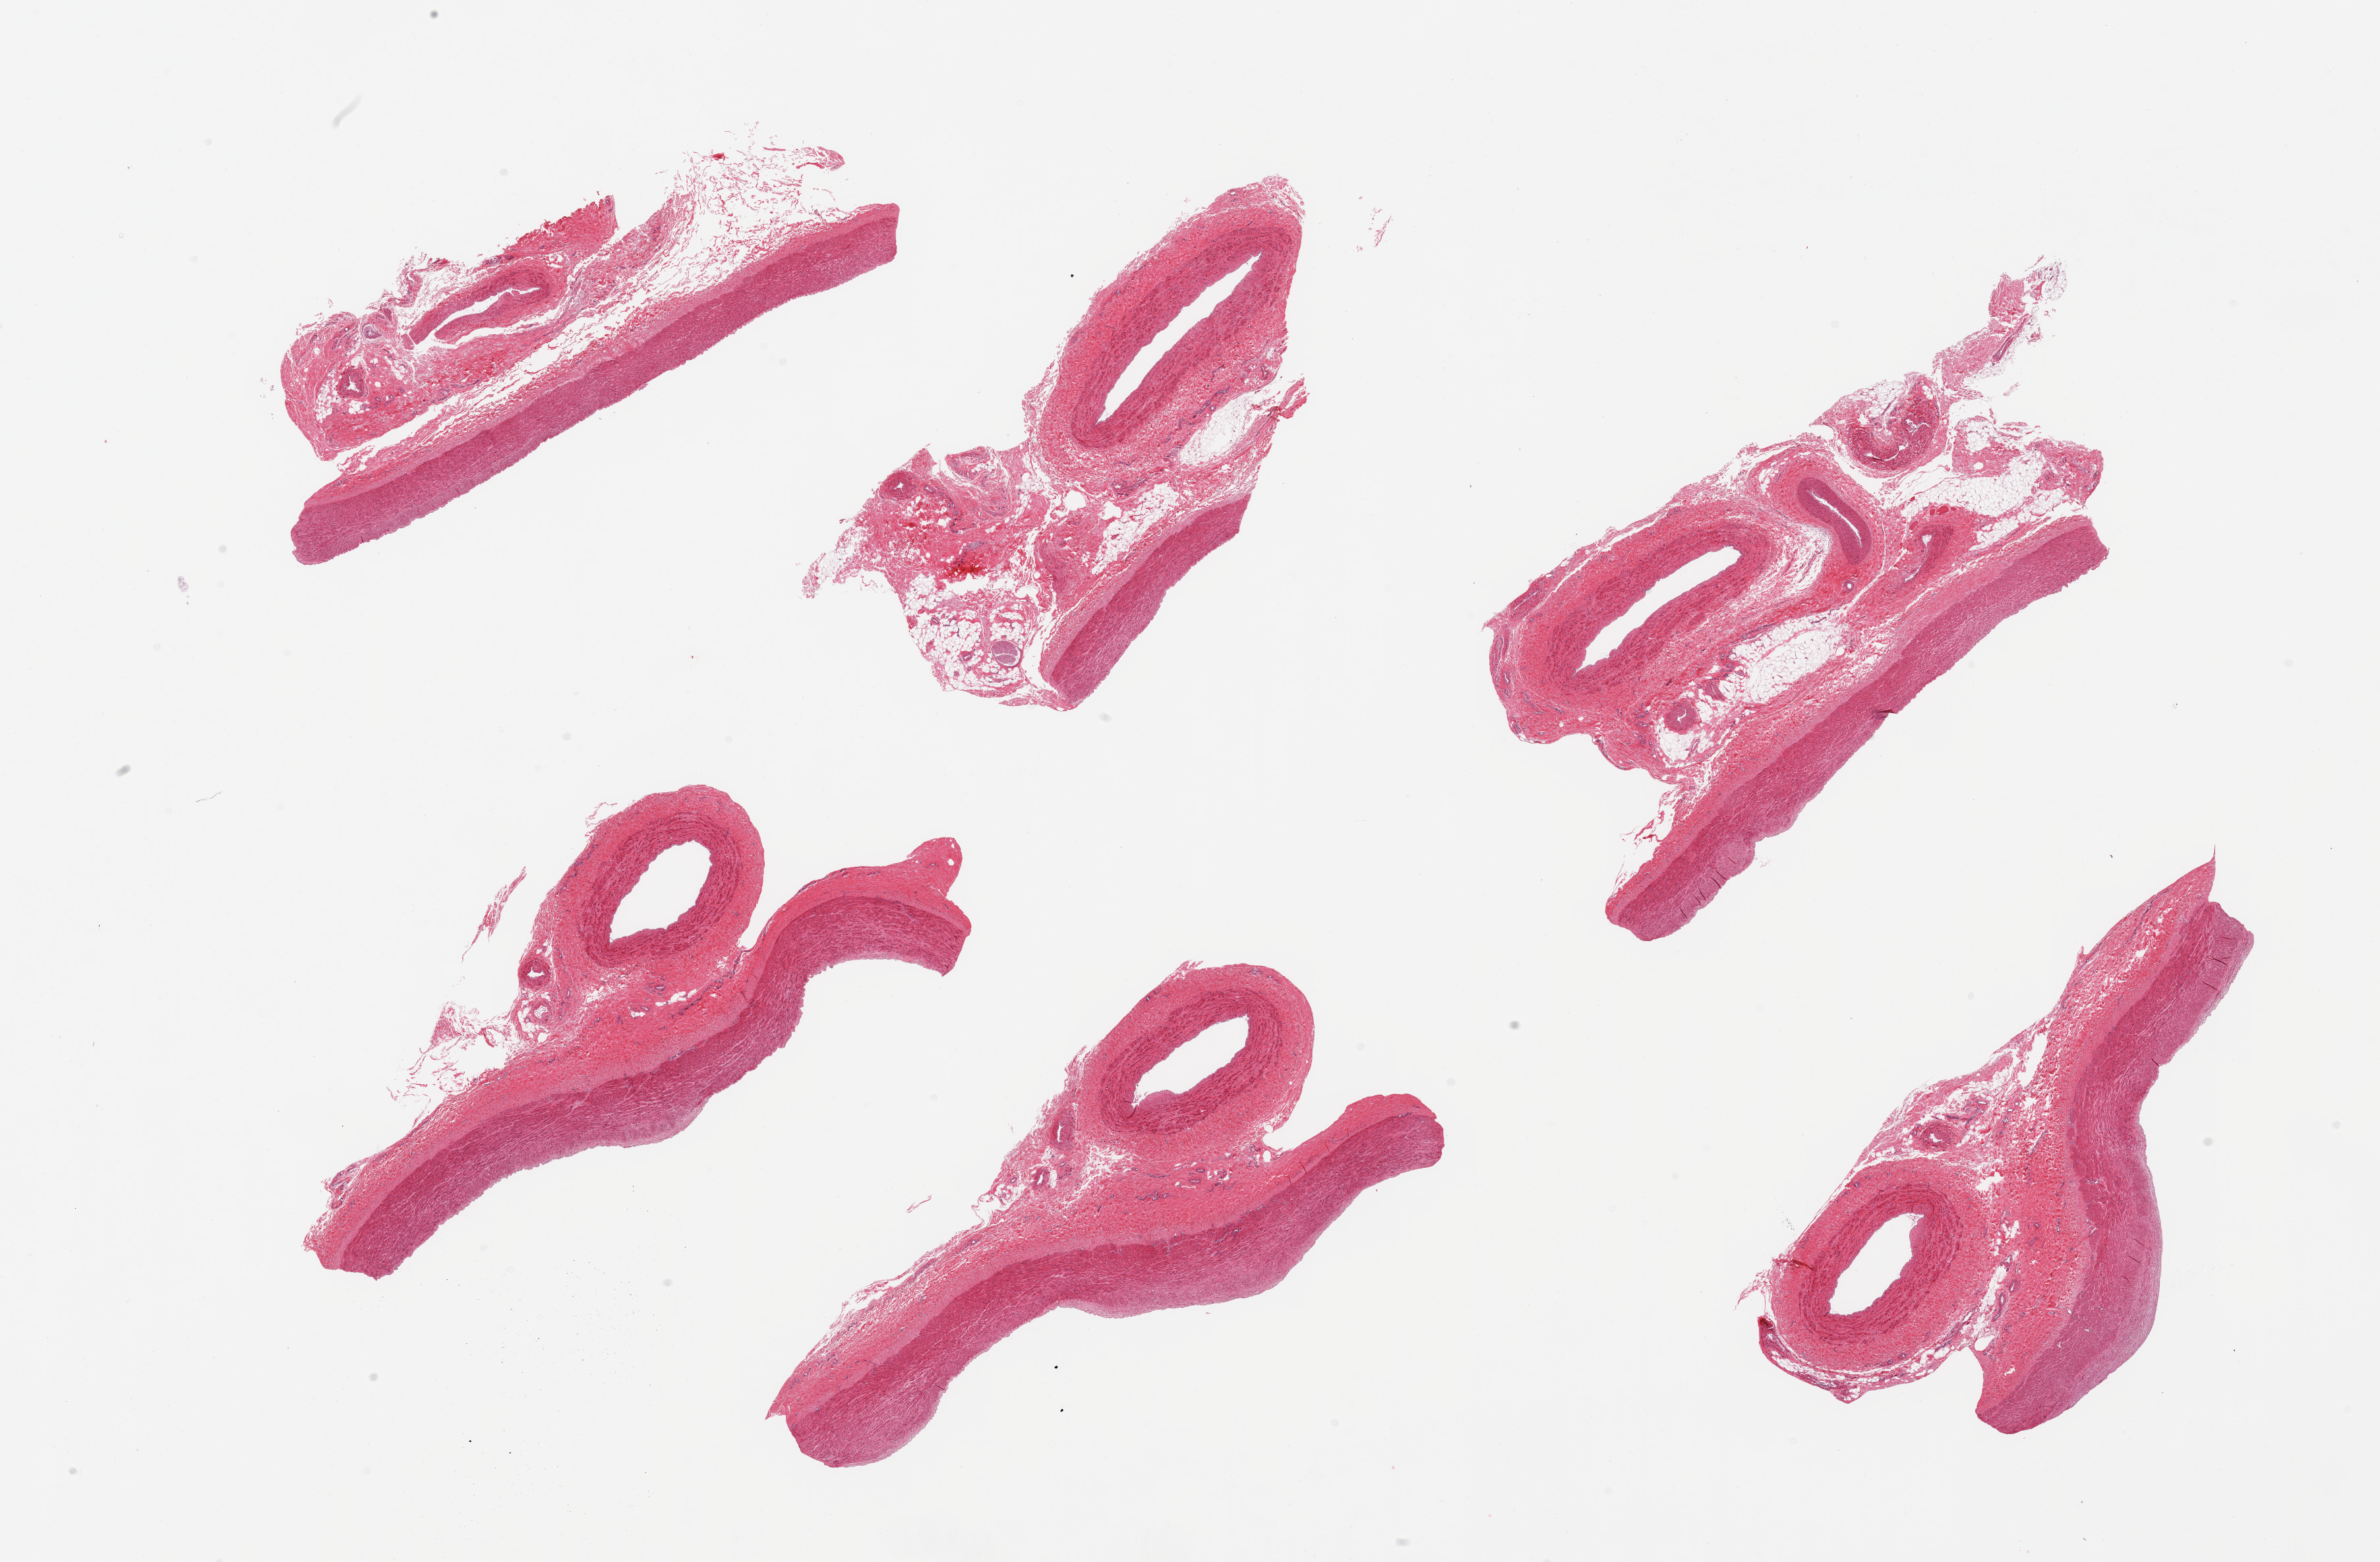
Digitized H&E-stained section, brightfield — low-resolution overview of the scanned area, about 28.5 x 18.7 mm (acquisition: 20x scan). PAXgene-fixed, paraffin-embedded tissue. Sampled site (target tissue): tibial artery. Donor tissue sample. Donor: male.
Pathologist's review note for this sample: 6 pieces; up to 30% perivascular fat.